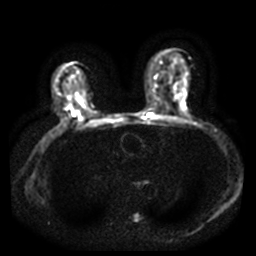
Breast MRI, one axial slice. Position 22 of 40 along the scan axis. Diffusion-weighted series; image 2 of 4 stored at this slice position (different b-values; order by instance number). 3 T. 5 mm slice thickness. 256 × 256 image matrix, field of view 360 × 360 mm. Female patient.
Outlined on this slice (manually delineated by an expert):
- tumour on diffusion-weighted imaging: bounding box [x1, y1, x2, y2] px = [73, 114, 75, 116]